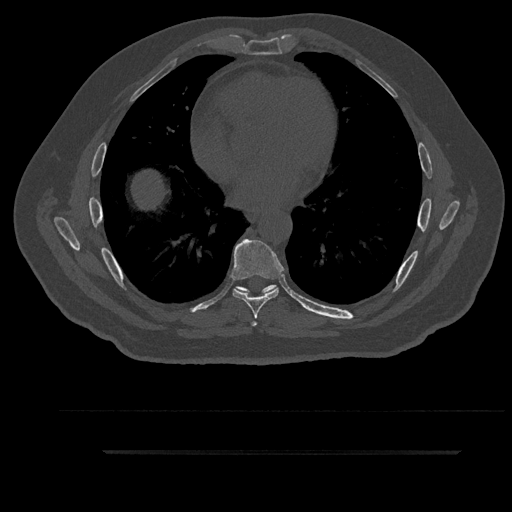
CT including the spine, one axial slice; slice 514 of 797 in the series (ordered by position); 120 kVp; bone window (W 1800 / L 400 HU); 0.5 mm slice thickness; 512 × 512 image matrix, field of view 432 × 432 mm. Patient: male, 63 years. Case-level facts recorded for this patient, not image findings: primary cancer: renal.
Outlined on this slice (semi-automatic segmentation, software-assisted and operator-edited):
- T6 vertebra: bounding box <235,287,269,326> (left, top, right, bottom; pixels)
- T7 vertebra: <232,239,285,319>
- T8 vertebra: <236,285,278,292>